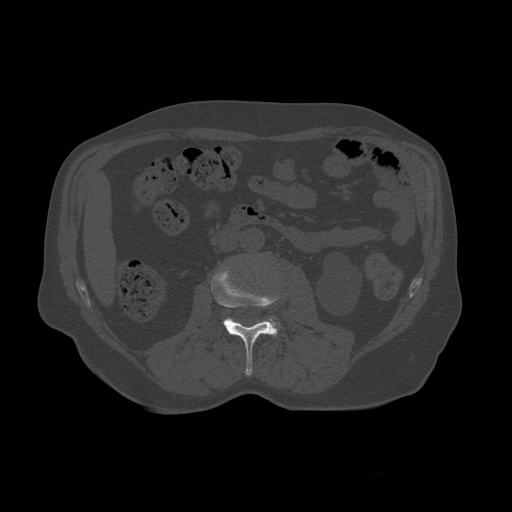
CT including the spine, one axial slice; slice 324 of 450 in the series (ordered by position); reconstruction kernel STANDARD; bone window (W 1800 / L 400 HU); 512 × 512 image matrix. Patient age 75 years. Case-level facts recorded for this patient, not image findings: primary cancer: prostate.
Annotated regions visible in this slice (semi-automatically segmented with operator editing):
- L2 vertebra: bounding box (x1, y1, x2, y2) in pixels: (211, 266, 280, 376)
- L3 vertebra: (269, 317, 281, 336)